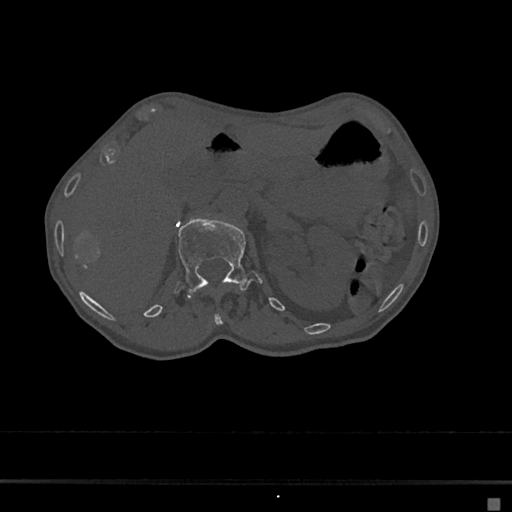
CT including the spine, one axial slice. Position 77 of 797 along the scan axis. Reconstruction kernel Br40s/3. 120 kVp. Bone window (W 1800 / L 400 HU). 0.5 mm slice thickness. 512 × 512 image matrix, field of view 360 × 360 mm. Female patient, age 68 years. From the clinical record (not read from this slice): primary cancer: renal.
Structures marked on this image (semi-automatically segmented with operator editing):
- L1 vertebra: box from (x=175, y=216) to (x=262, y=297) px
- T12 vertebra: (x=212, y=312)–(x=223, y=326)